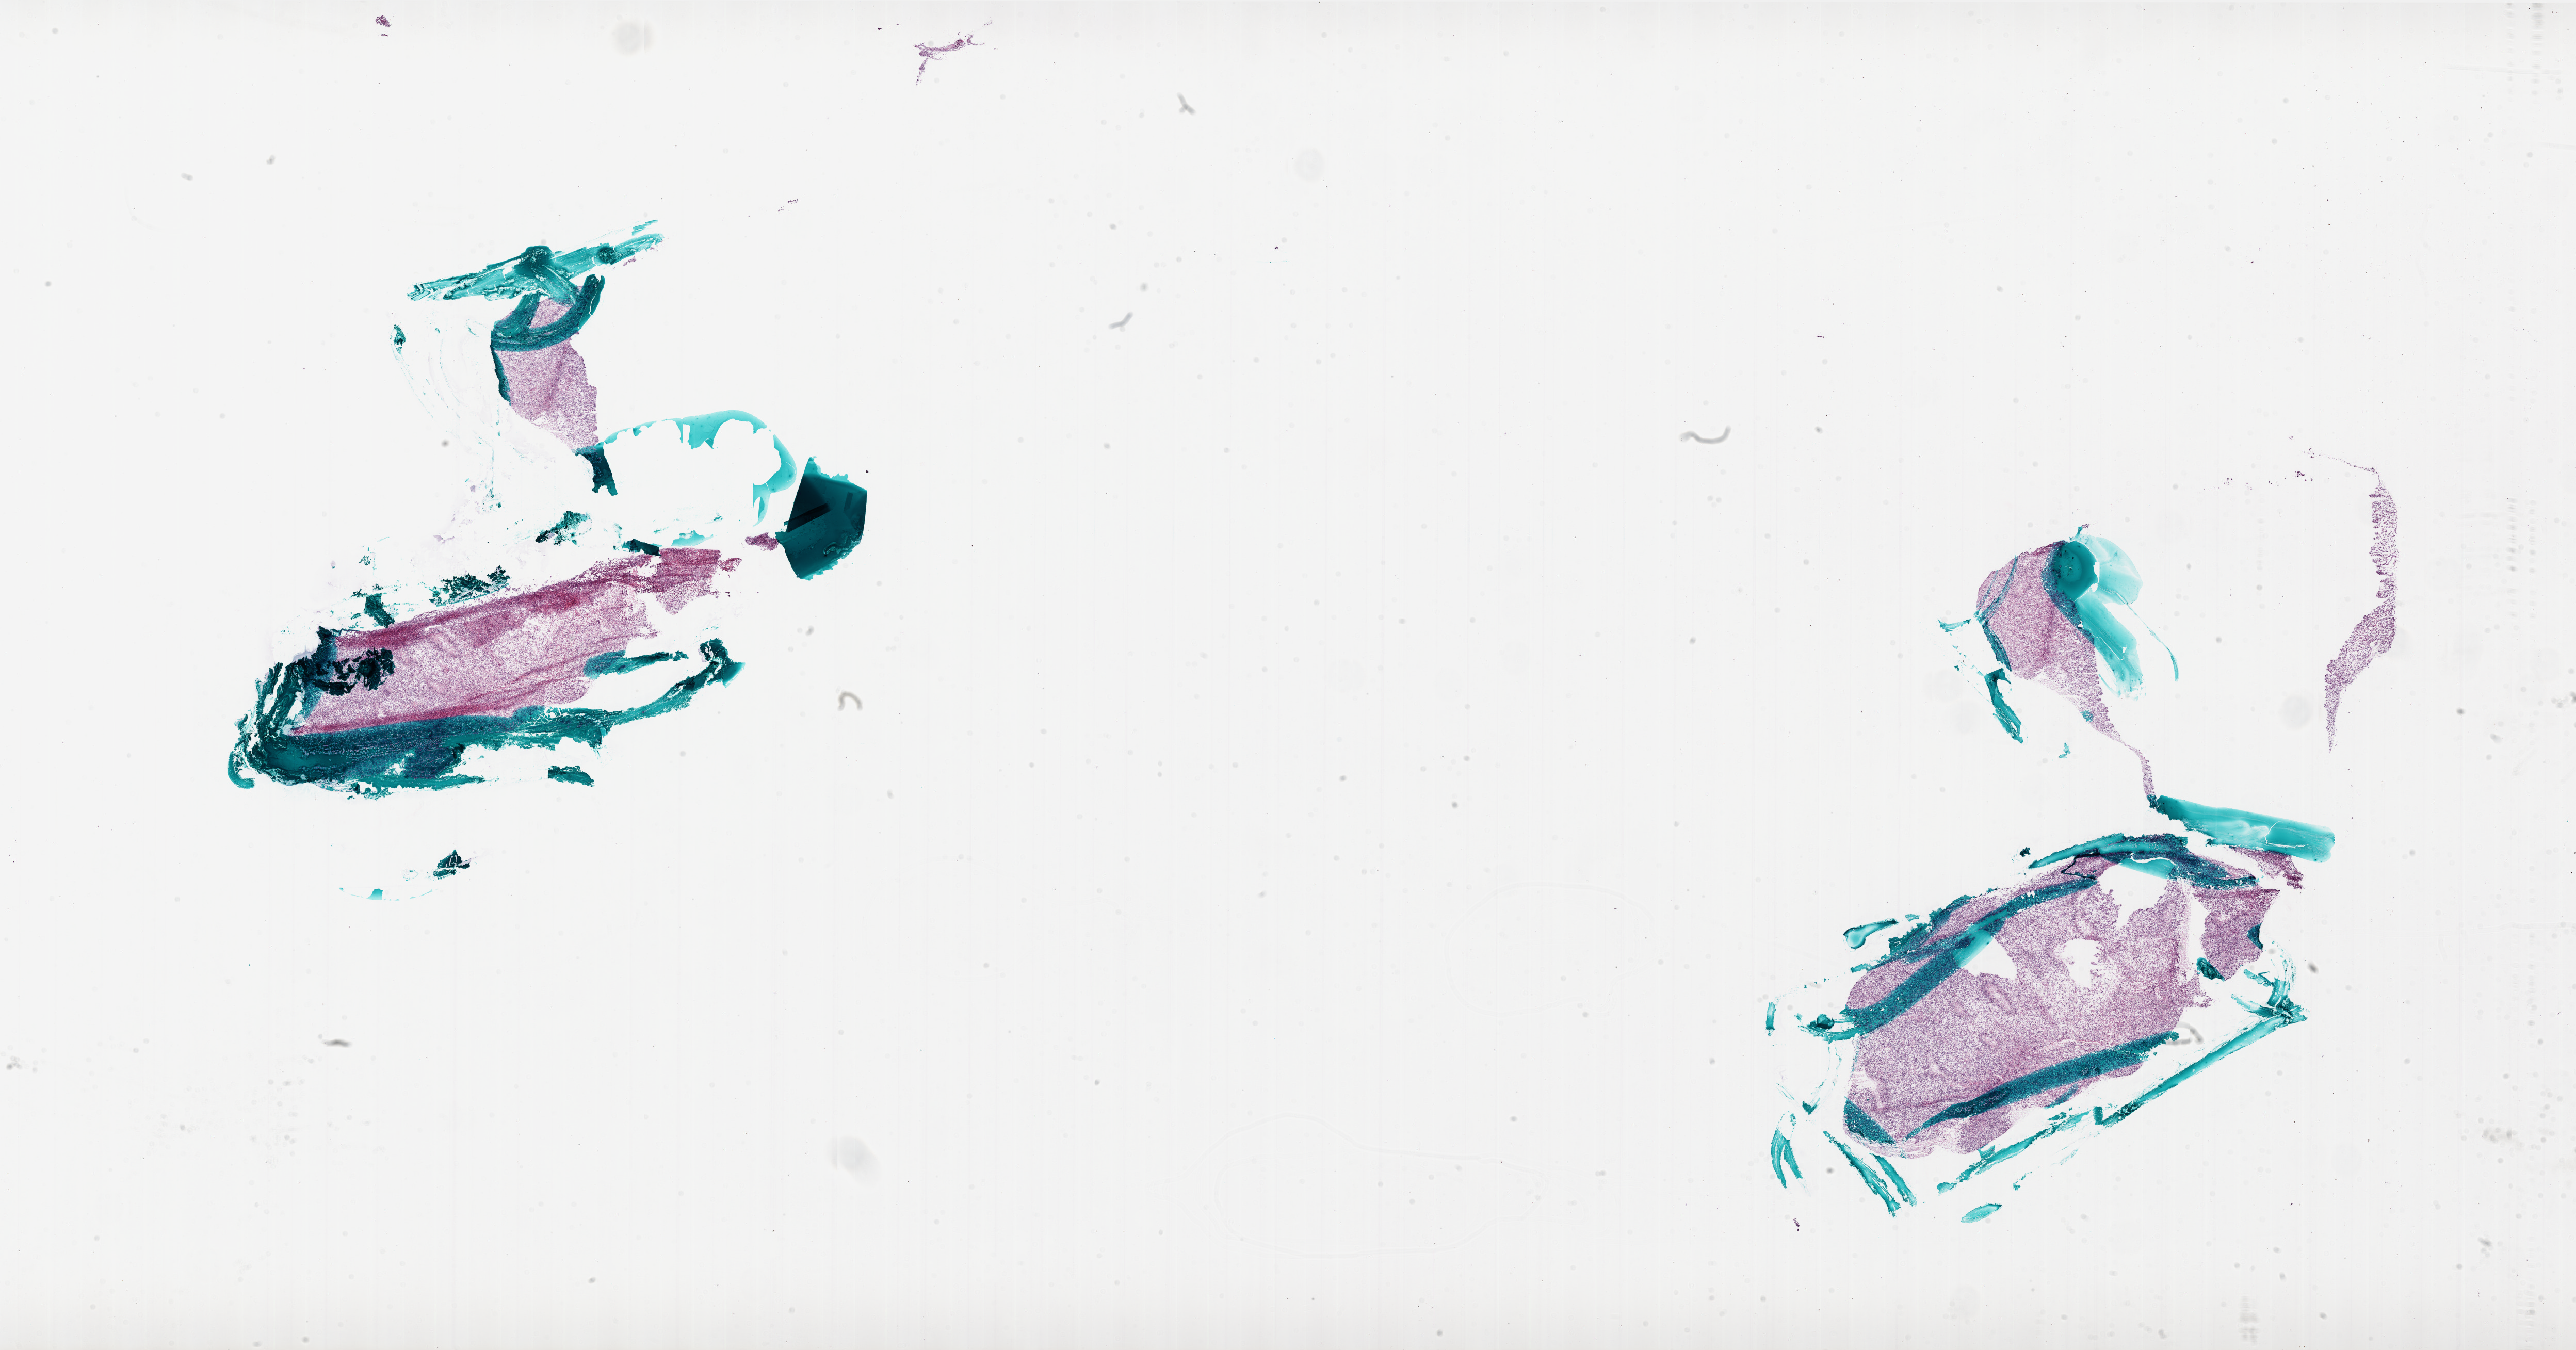
Digitized H&E tissue section (whole slide) — low-resolution overview of the scanned area, about 40.0 x 20.9 mm, frozen section from the bottom of the tissue portion, primary tumour sample from the brain. Patient: female, age at initial diagnosis 37 years. Composition of this section per pathologist review: tumour cells 85%, tumour nuclei 100%, normal cells 0%, stromal cells 0%, necrosis 15%.
• diagnosis: Glioblastoma